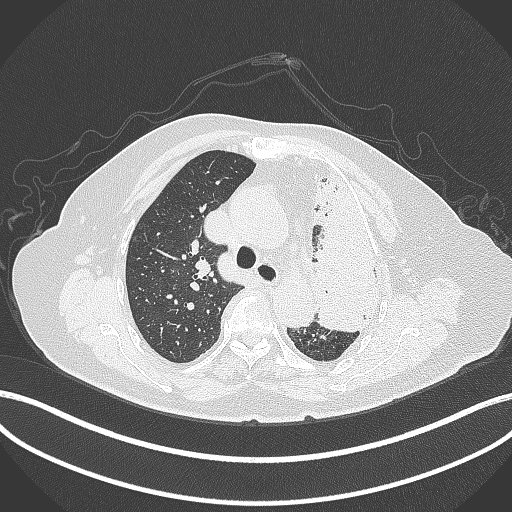
Chest CT, one axial slice. Position 279 of 399 along the scan axis. Reconstruction kernel B70f. 120 kVp. Lung window (W 1500 / L -600 HU). 1 mm slice thickness. 512 × 512 image matrix, field of view 400 × 400 mm. Patient: female, 75 years. Case-level facts recorded for this patient, not image findings: clinical TNM (as recorded): T3 N3 M1.
Annotated regions visible in this slice (rectangle marked by the reading radiologist):
- lung tumour (recorded histology: adenocarcinoma): bounding box [x1, y1, x2, y2] px = [307, 163, 383, 336]